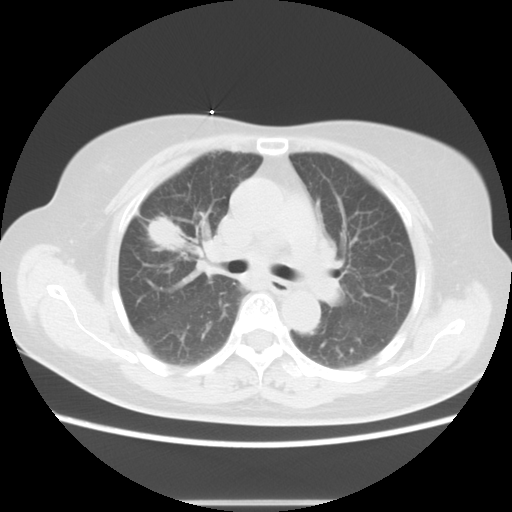
Chest CT, one axial slice; position 8 of 17 along the scan axis; reconstruction kernel STANDARD; 120 kVp; lung window (W 1500 / L -600 HU); 5 mm slice thickness; 512 × 512 image matrix, field of view 350 × 350 mm. Patient: female, 57 years. From the clinical record (not read from this slice): clinical TNM (as recorded): T1c N1 M0.
Annotated regions visible in this slice (bounding box drawn by a radiologist):
- lung tumour (recorded histology: adenocarcinoma): box from (x=145, y=208) to (x=191, y=257) px